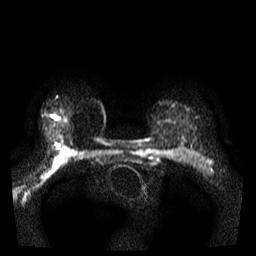
Breast MRI, one axial slice. Position 26 of 35 along the scan axis. Diffusion-weighted series; image 2 of 4 stored at this slice position (different b-values; order by instance number). 3 T. 256 × 256 image matrix, field of view 300 × 300 mm. Female patient.
Outlined on this slice (expert manual segmentation):
- tumour on diffusion-weighted imaging: box from (x=54, y=117) to (x=56, y=119) px